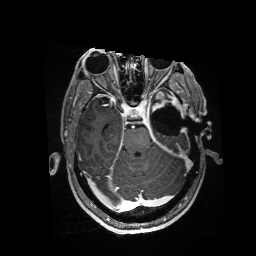
Brain MRI from a brain-tumour surgery series, one axial slice; slice 108 of 176 in the series (ordered by position); T1-weighted post-contrast; 256 × 256 image matrix, field of view 256 × 256 mm. From the clinical record (not read from this slice): histopathology: Glioblastoma; WHO grade: 4; IDH mutation: no; tumour location: Left Anterior/Superior Temporal.
Structures marked on this image (outlined manually by an expert reader):
- residual tumour: bounding box <152,92,184,118> (left, top, right, bottom; pixels)